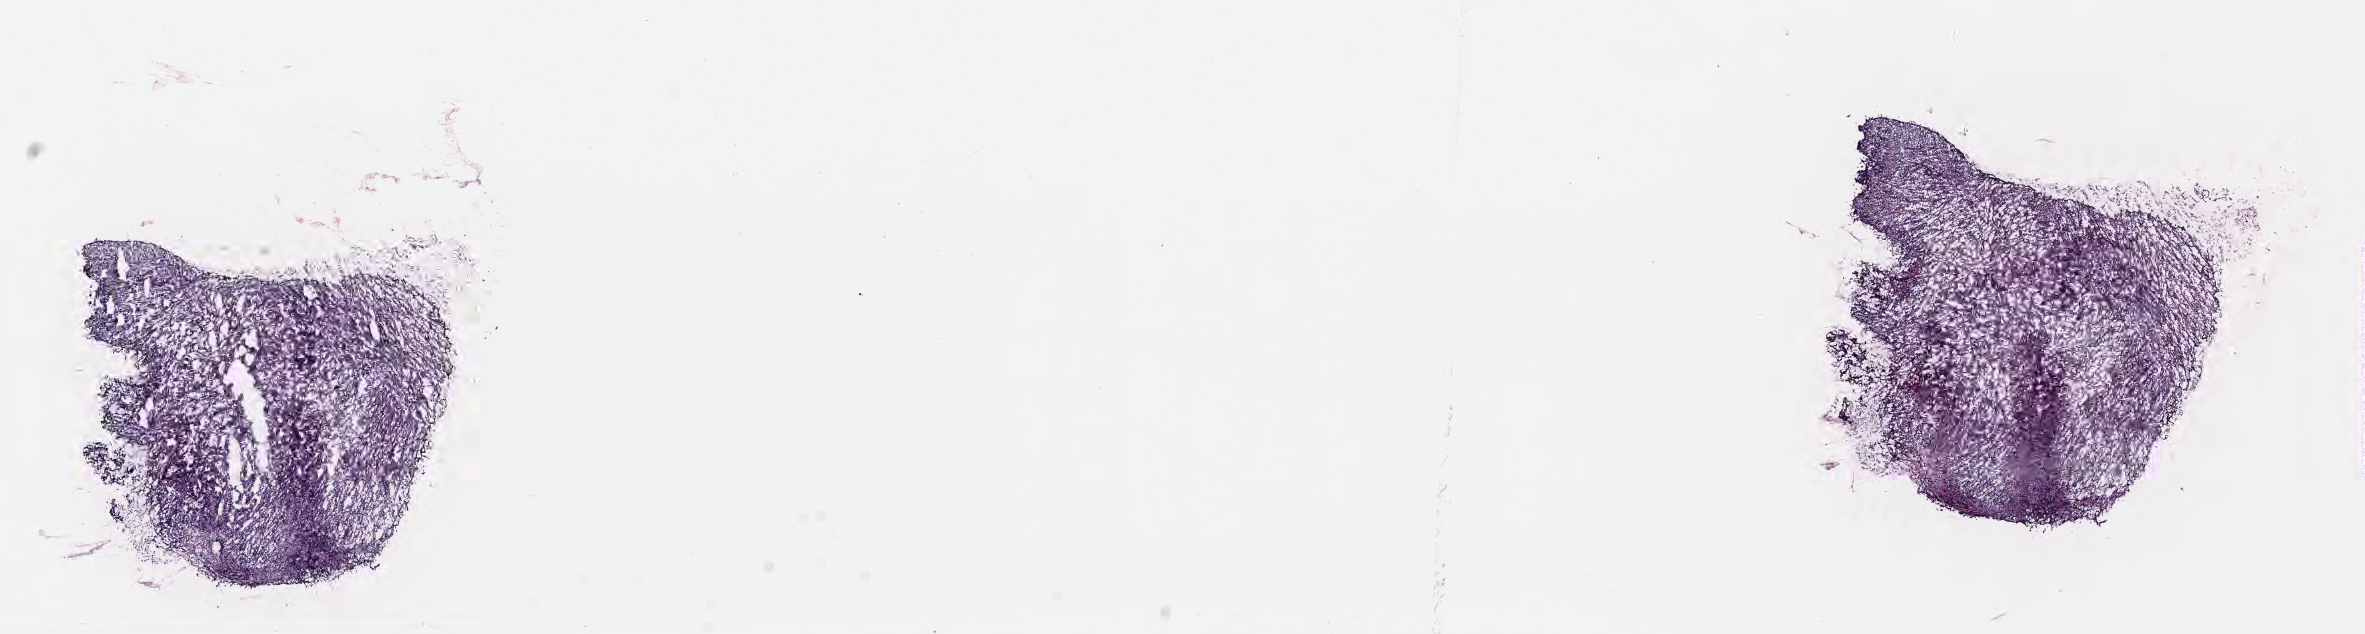
Whole-slide image, H&E stain, a low-resolution overview of the entire scanned area, about 19.1 x 5.1 mm, frozen section, specimen: primary tumor, anatomic site: soft tissue of abdomen. Patient: female, age at initial diagnosis 8 years.
Diagnosis: Burkitt lymphoma, NOS.